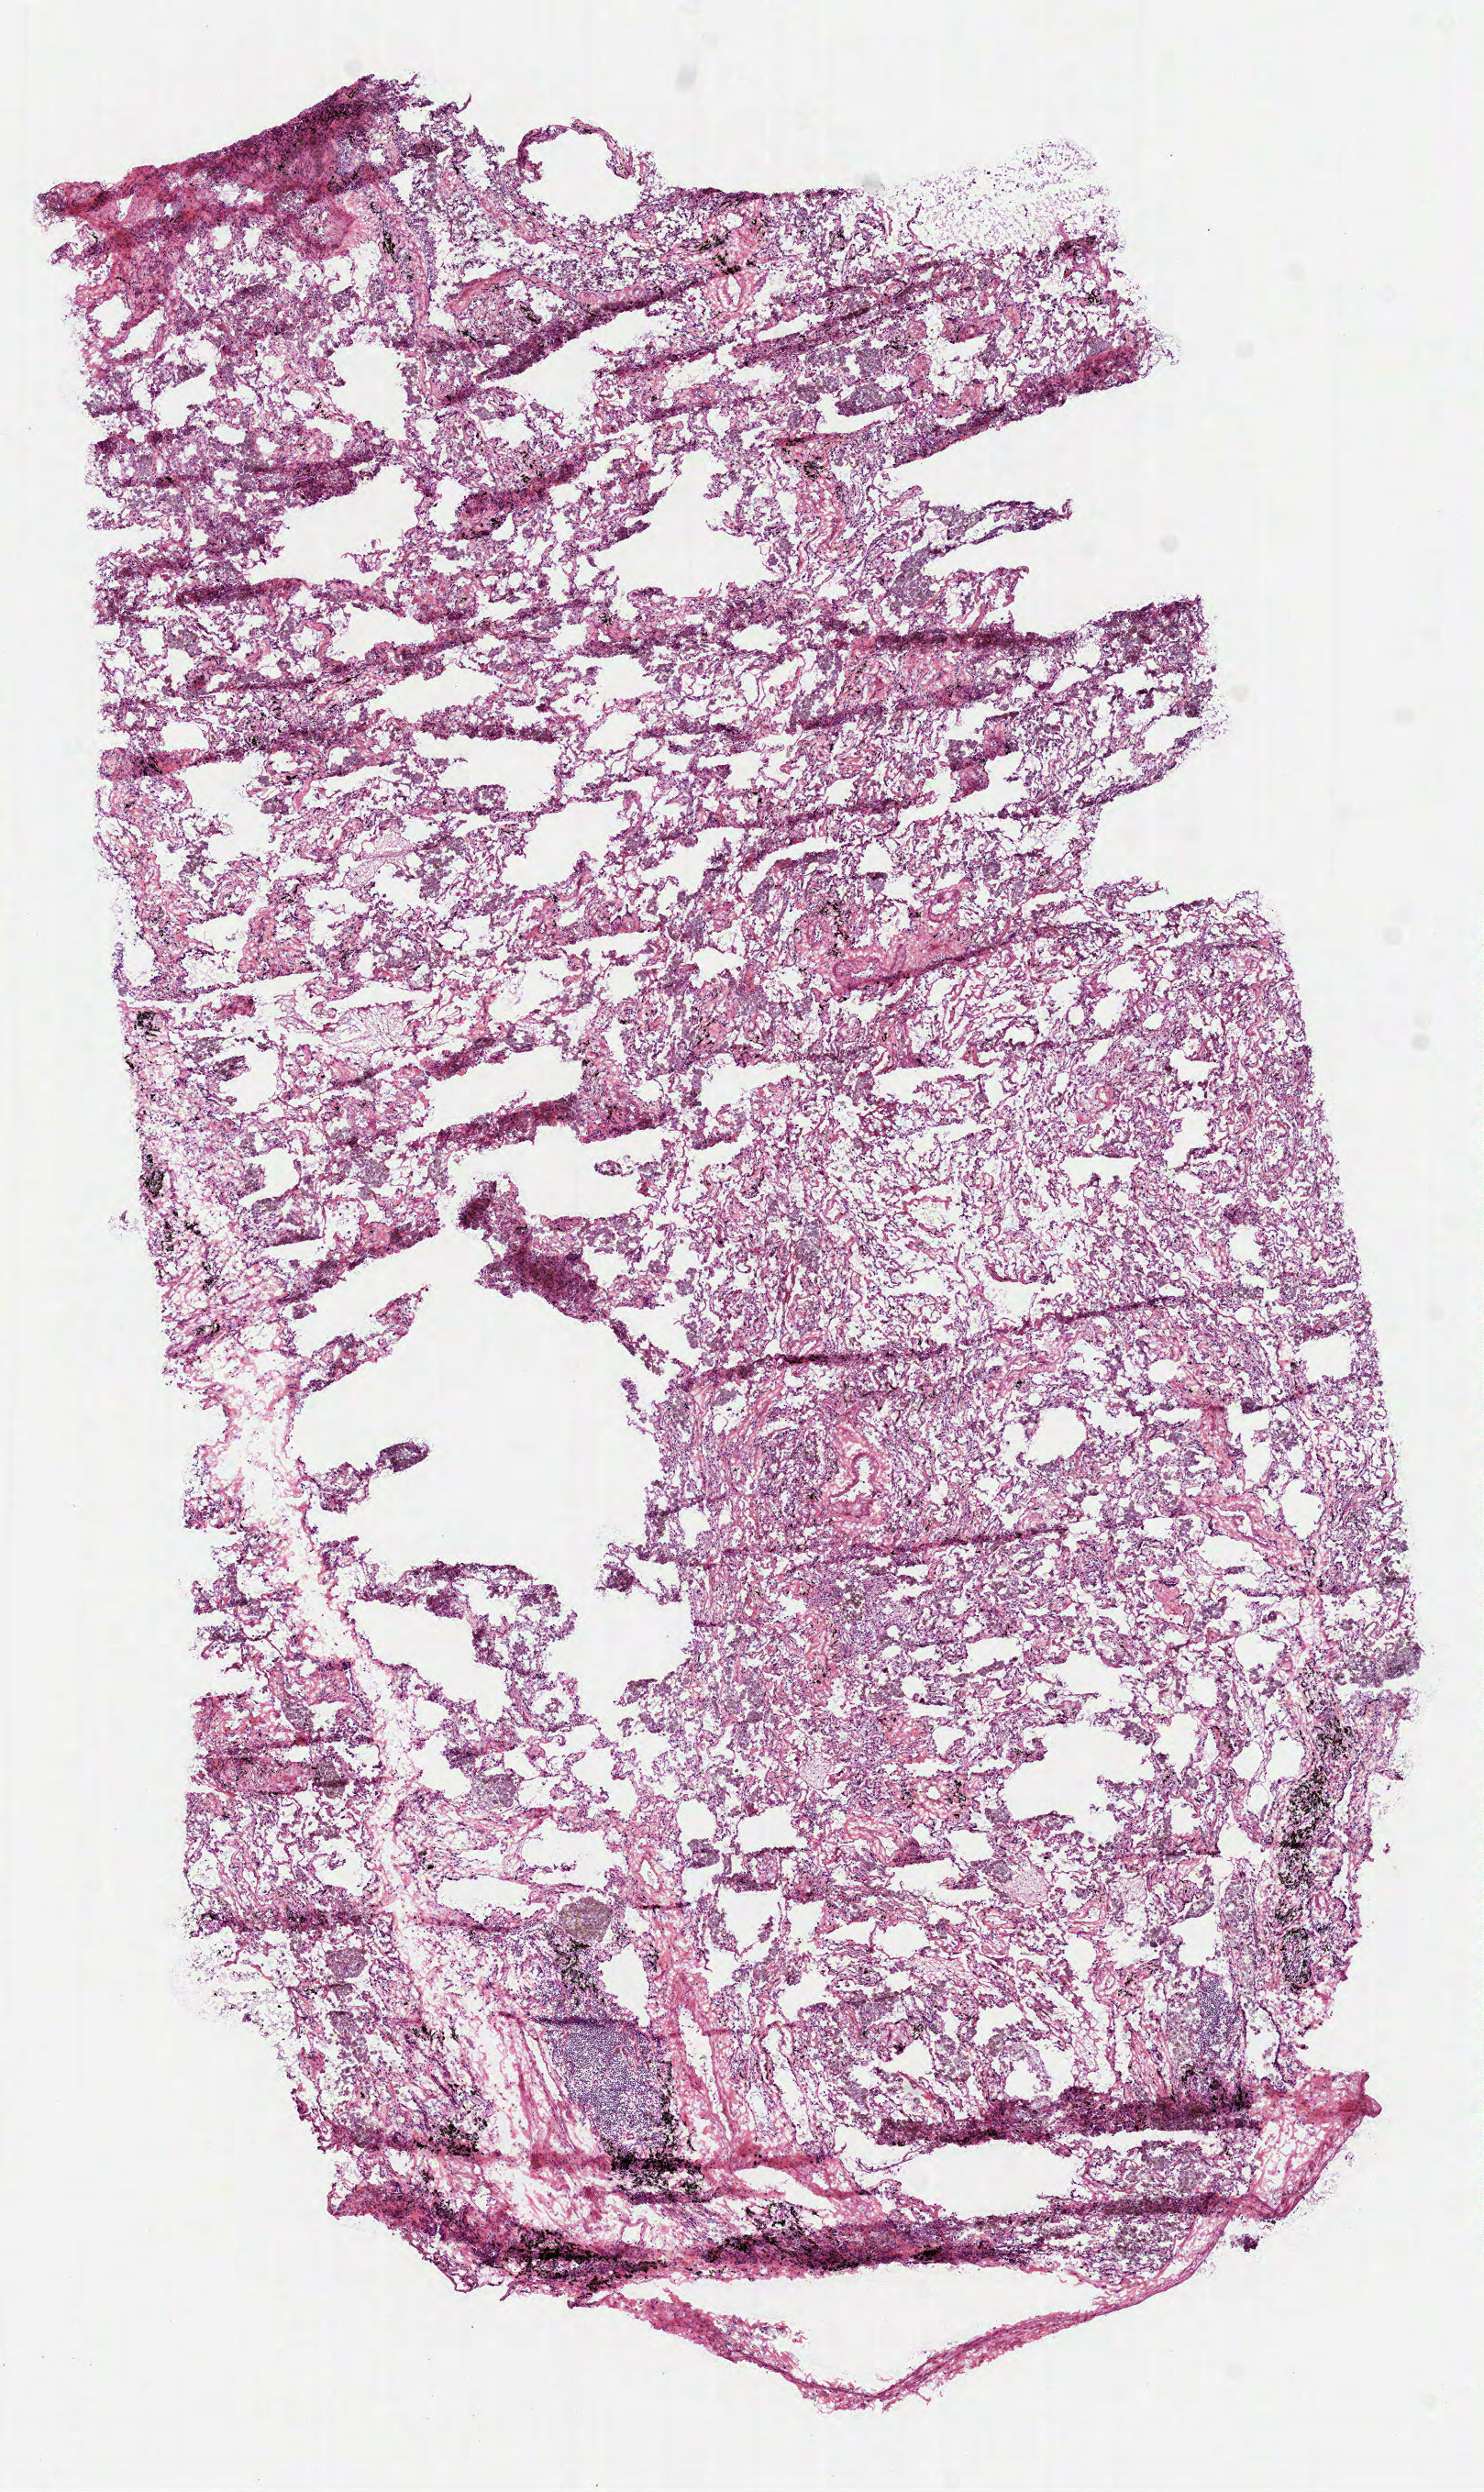
H&E whole-slide image — low-resolution overview of the scanned area, about 6.5 x 11.0 mm; frozen section; sample: solid tissue normal (non-tumour tissue), lung. Male patient; age at initial diagnosis 60 years.
* this section: solid tissue normal (non-tumour) sample from the same patient
* patient diagnosis: Adenocarcinoma, NOS (upper lobe, lung)